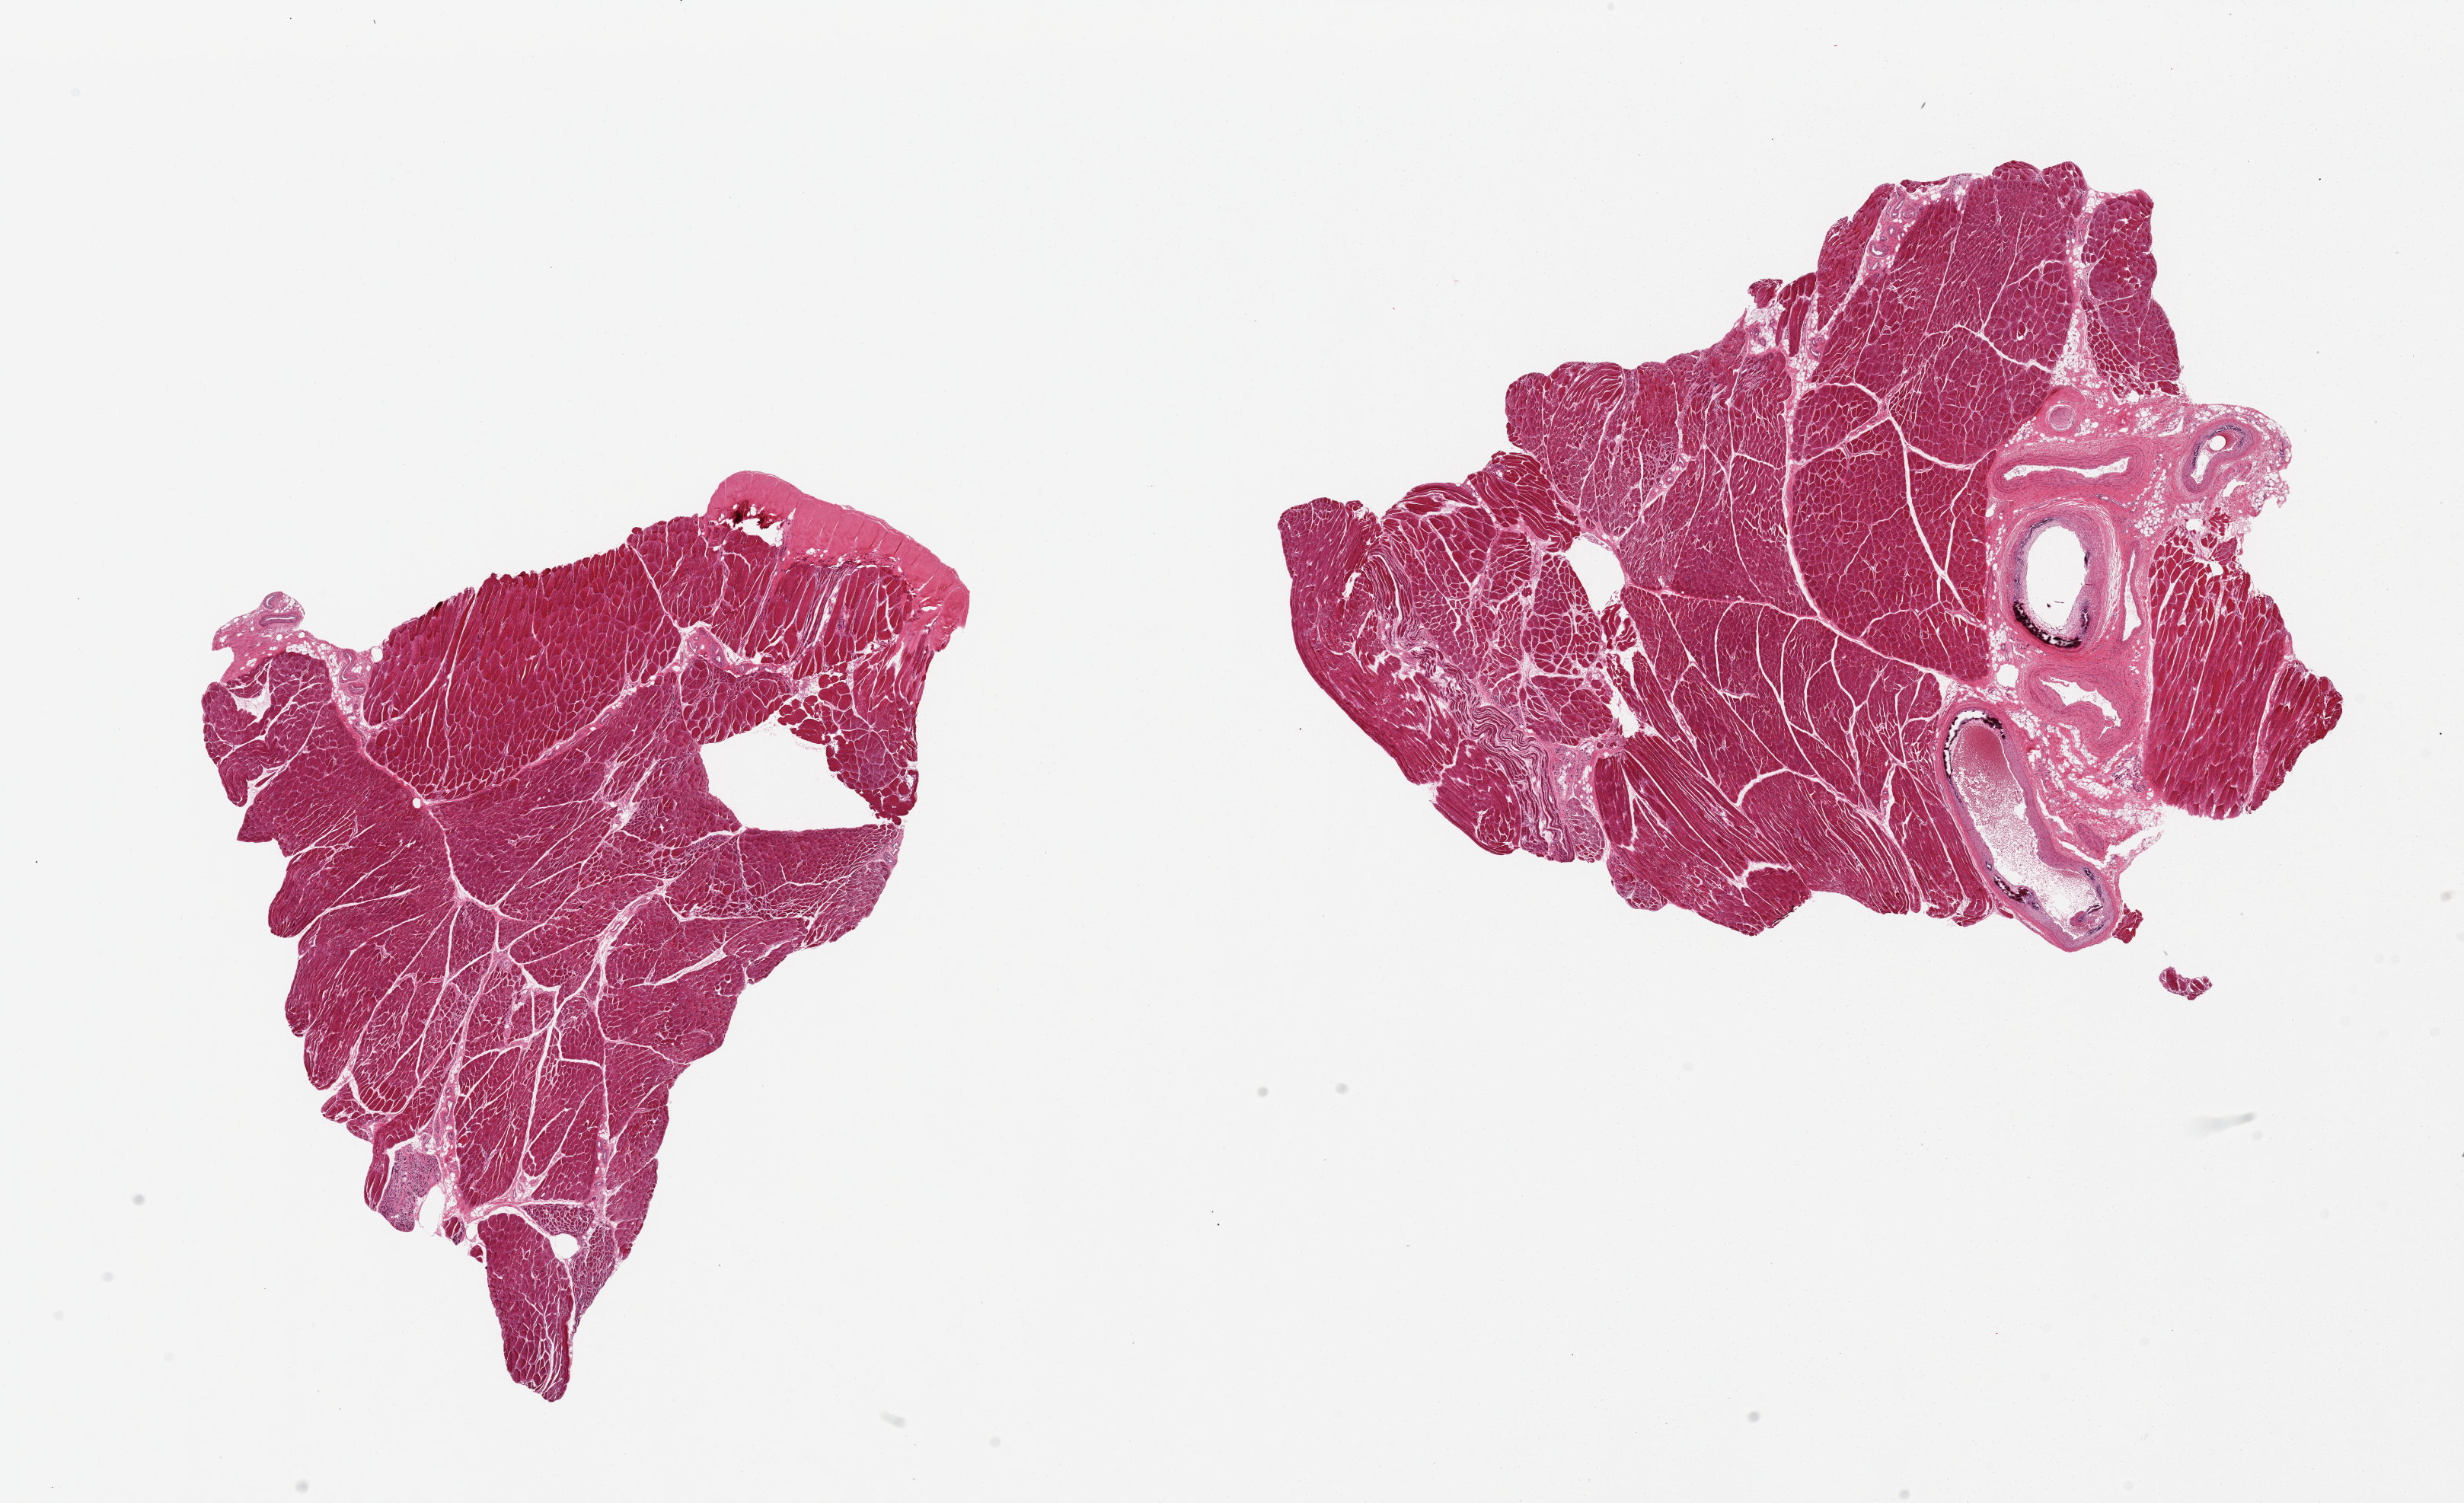
Hematoxylin and eosin (H&E) whole-slide image — a low-resolution overview of the entire scanned area, about 25.6 x 15.6 mm (from a 20x scan). PAXgene-fixed, paraffin-embedded tissue. Section of skeletal muscle (target tissue). Donor tissue sample. Donor sex: male.
Pathologist's review note for this sample: 2 pieces, with tendon and several large vessels attached (encompasses ~10% of tissue). Medial calcific sclerosis of vessels. Patchy atrophy of skeletal muscle.